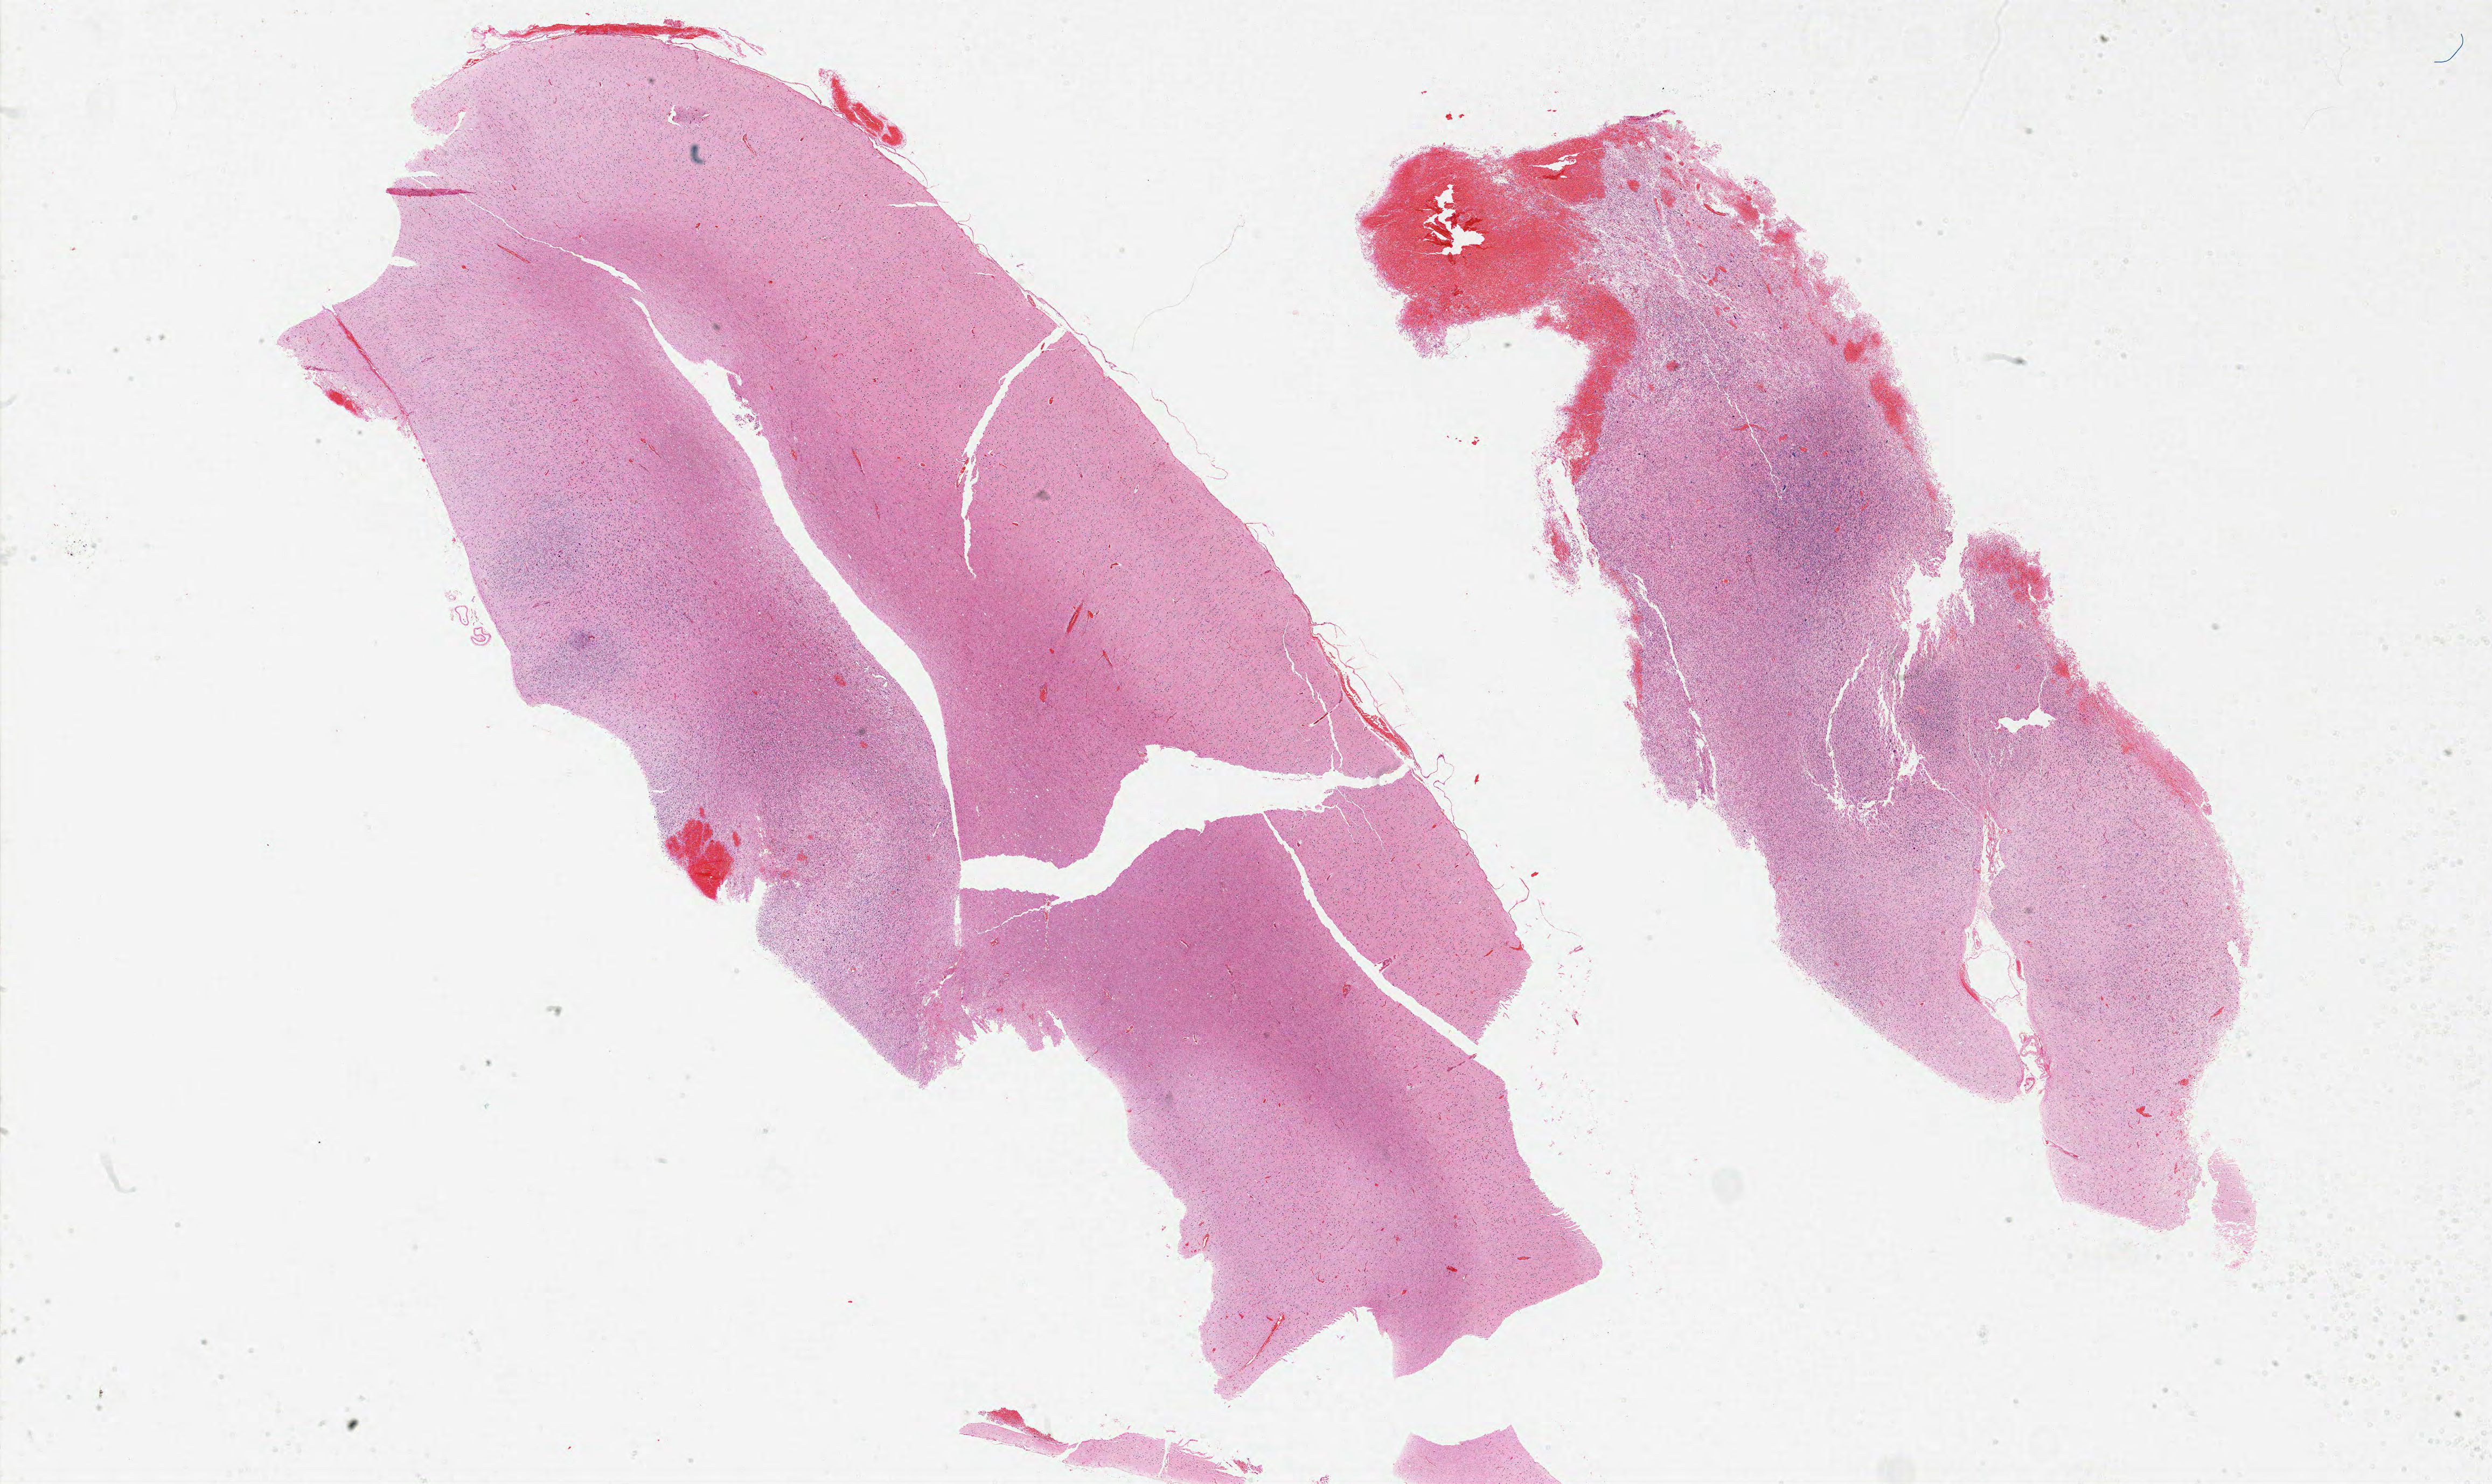
Digitized Hematoxylin and eosin (H&E) stained tissue section (whole slide) — shown as a low-resolution overview of the whole scanned area (about 37.0 x 22.0 mm, from a 20x scan); FFPE section; brain, primary tumour sample. Male patient; age at initial diagnosis 51 years.
Histologic diagnosis: Glioblastoma.